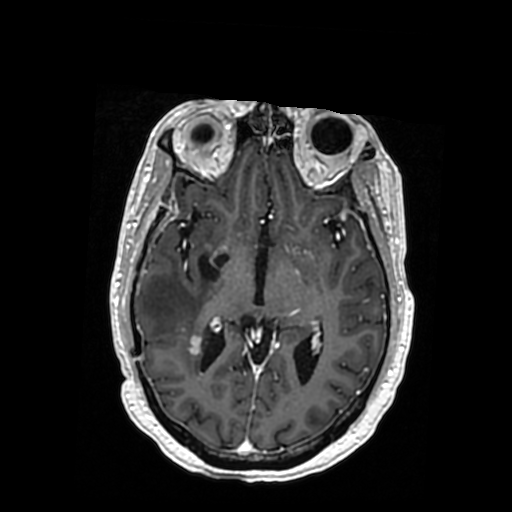
Brain MRI from a brain-tumour surgery series, one axial slice; position 195 of 364 along the scan axis; T1-weighted post-contrast; 0.5 mm slice thickness; 512 × 512 image matrix, field of view 260 × 260 mm. Case-level facts recorded for this patient, not image findings: histopathology: Oligodendroglioma; WHO grade: 3; IDH mutation: yes.
Outlined on this slice (expert manual segmentation):
- previous resection cavity: bounding box [x1, y1, x2, y2] px = [198, 253, 228, 281]
- tumour: [176, 333, 189, 351]